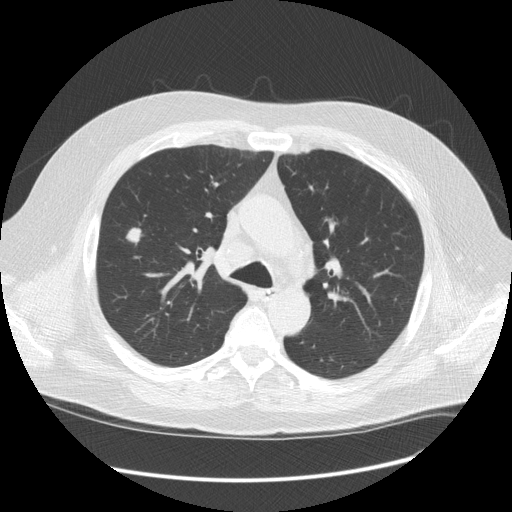
Axial slice from a low-dose chest CT screening exam. Third annual screen. Lung window (W 1500 / L -600 HU). 2.5 mm slice thickness. 120 kVp. Slice 41 of 128 in the series. 512 × 512 image matrix. Male participant, aged 61 years at enrolment.
Expert reader's lesion annotation, bounding box <107,218,151,257> (left, top, right, bottom; pixels). The exam's reader record, not a measurement of the box and not confirmed to be the same lesion: non-calcified nodule or mass ≥4 mm, right upper lobe, 13 × 11 mm, spiculated (stellate) margins, soft tissue attenuation, pre-existing on the prior screen: yes; interval growth: yes. Lung cancer was diagnosed 21 days after this screen: adenocarcinoma, NOS, right upper lobe, stage IIIA (AJCC 6th edition), 13 mm at pathology.